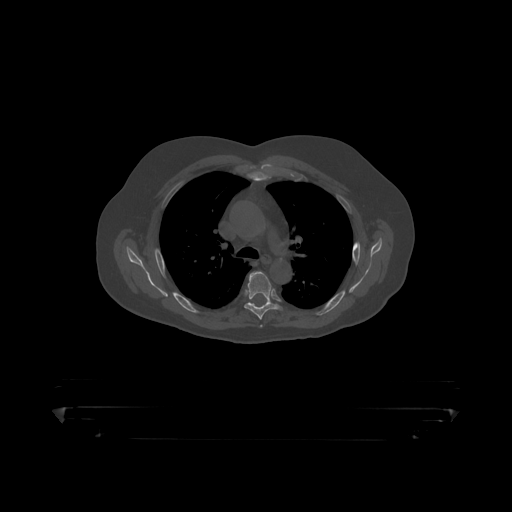
CT including the spine, one axial slice; position 321 of 390 along the scan axis; reconstruction kernel STANDARD; 120 kVp; bone window (W 1800 / L 400 HU); 1.25 mm slice thickness; 512 × 512 image matrix, field of view 650 × 650 mm. Male patient, age 60 years. From the clinical record (not read from this slice): primary cancer: prostate.
Annotated regions visible in this slice (semi-automatic segmentation, software-assisted and operator-edited):
- T5 vertebra: bounding box <245,272,280,319> (left, top, right, bottom; pixels)
- T6 vertebra: <252,302,272,307>